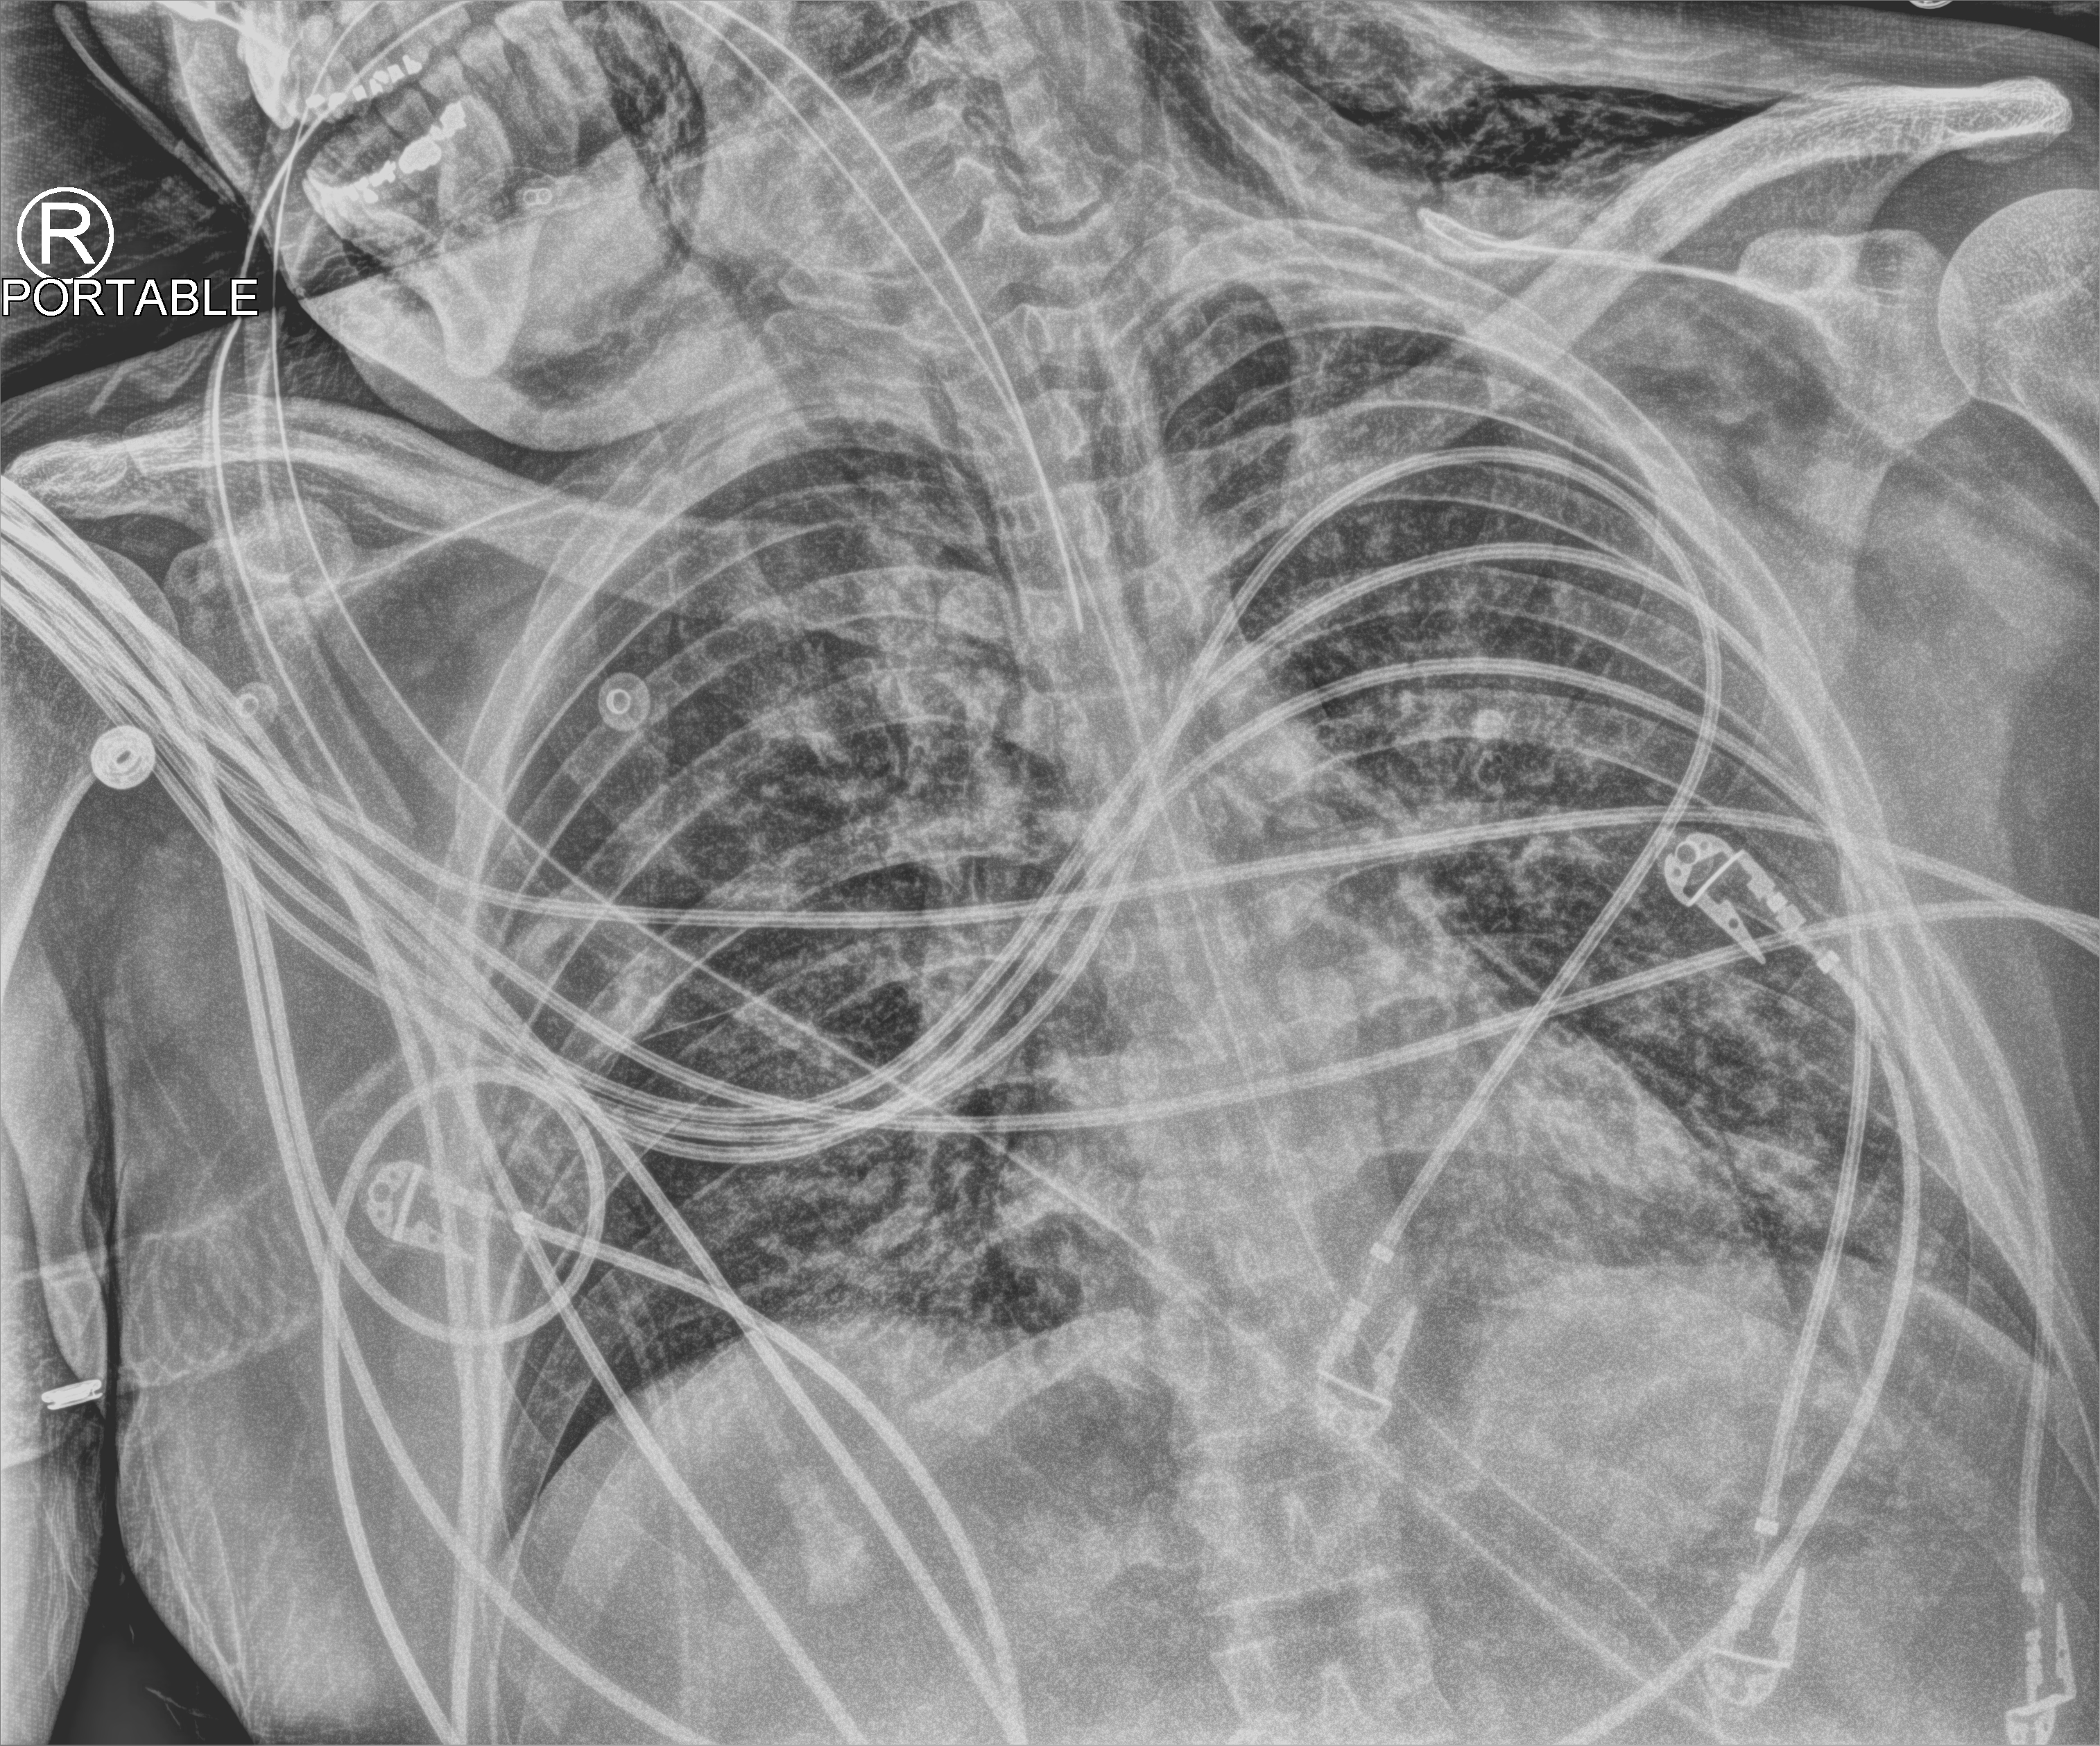
Portable chest radiograph; anteroposterior (AP) projection. Adult patient hospitalised with COVID-19, age 18–59 years.
Hospital-stay facts (about this admission, not read from this image; timing relative to this image not recorded): length of hospital stay: 60 days; admitted to intensive care during this hospital stay: yes; mechanically ventilated during this hospital stay: yes.